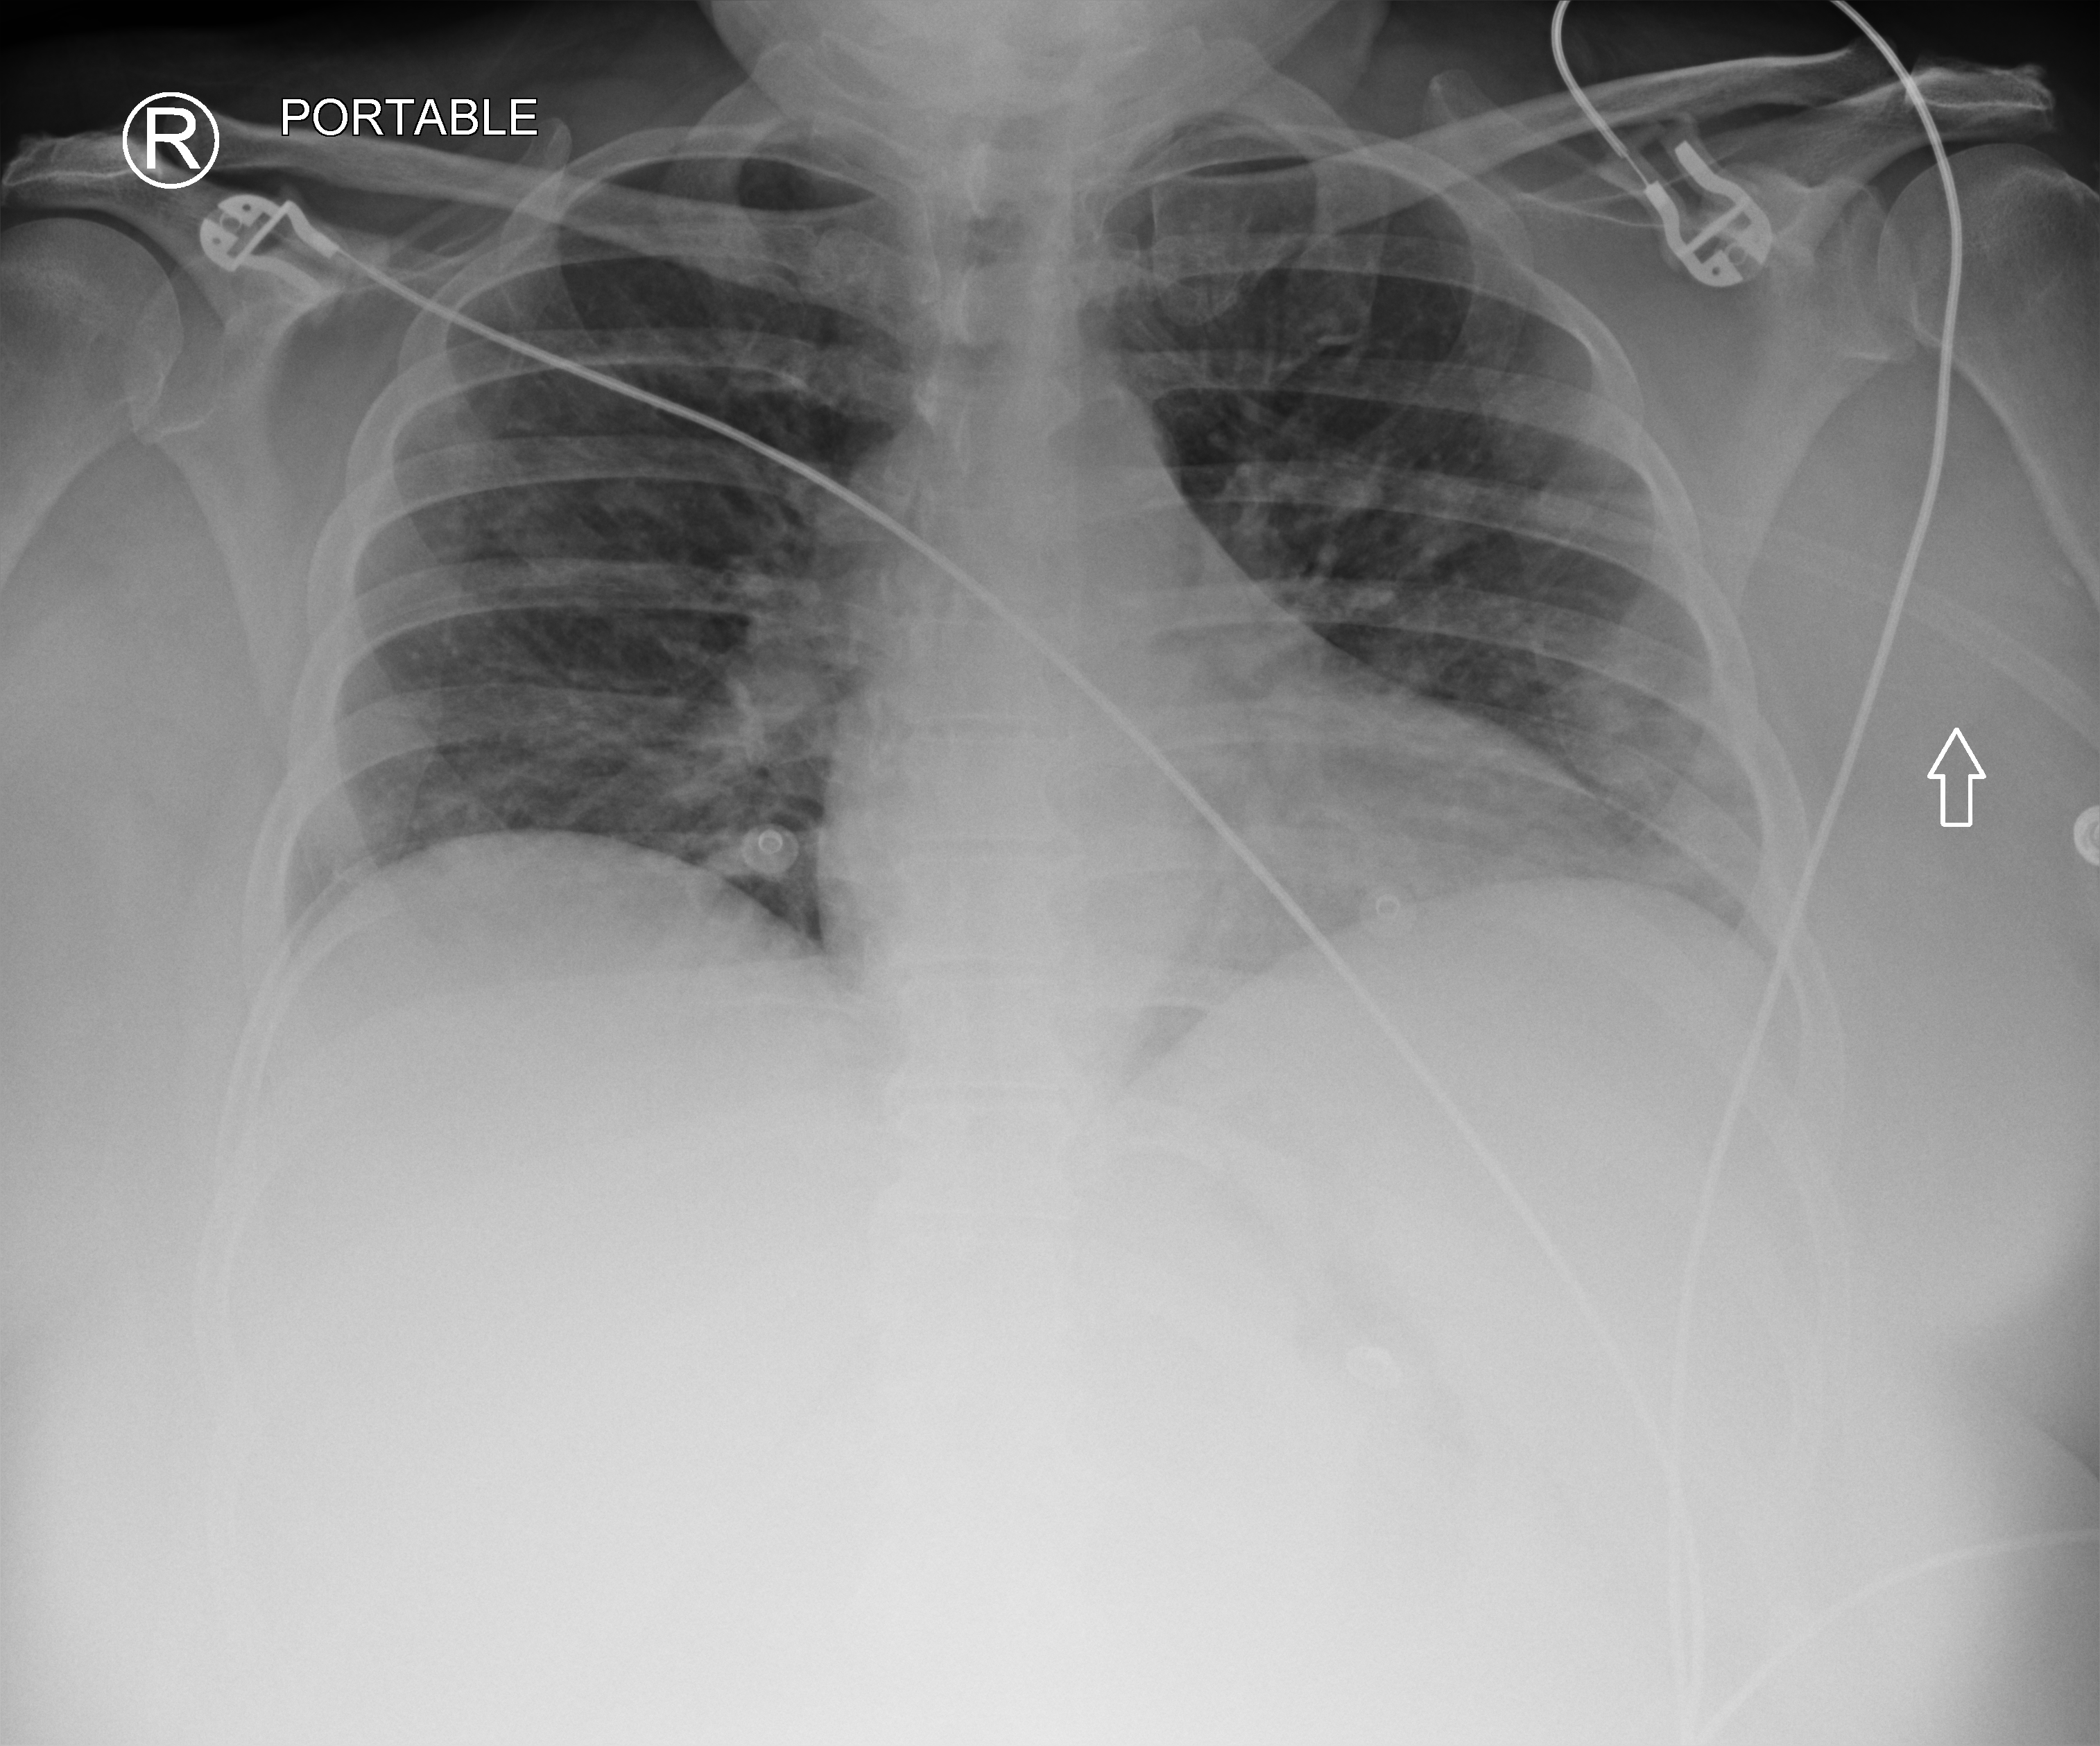
Portable chest radiograph; anteroposterior (AP) projection. Patient hospitalised with COVID-19; female, aged 18–59 years.
Hospital-stay facts (about this admission, not read from this image; timing relative to this image not recorded): smoking status (admission record): never; hypertension (admission record): yes; mechanically ventilated during this hospital stay: no.